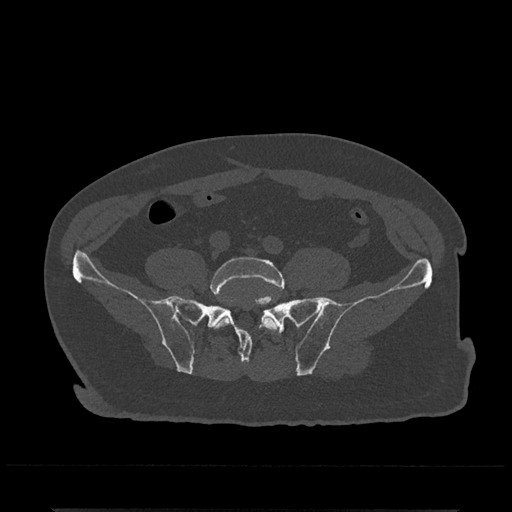
CT including the spine, one axial slice. Slice 53 of 797 in the series (ordered by position). Reconstruction kernel Br40s/3. Bone window (W 1800 / L 400 HU). 0.5 mm slice thickness. 512 × 512 image matrix. Male patient, age 67 years. Case-level facts recorded for this patient, not image findings: primary cancer: prostate.
Structures marked on this image (semi-automatic segmentation, software-assisted and operator-edited):
- L5 vertebra: bounding box [x1, y1, x2, y2] px = [210, 257, 284, 332]